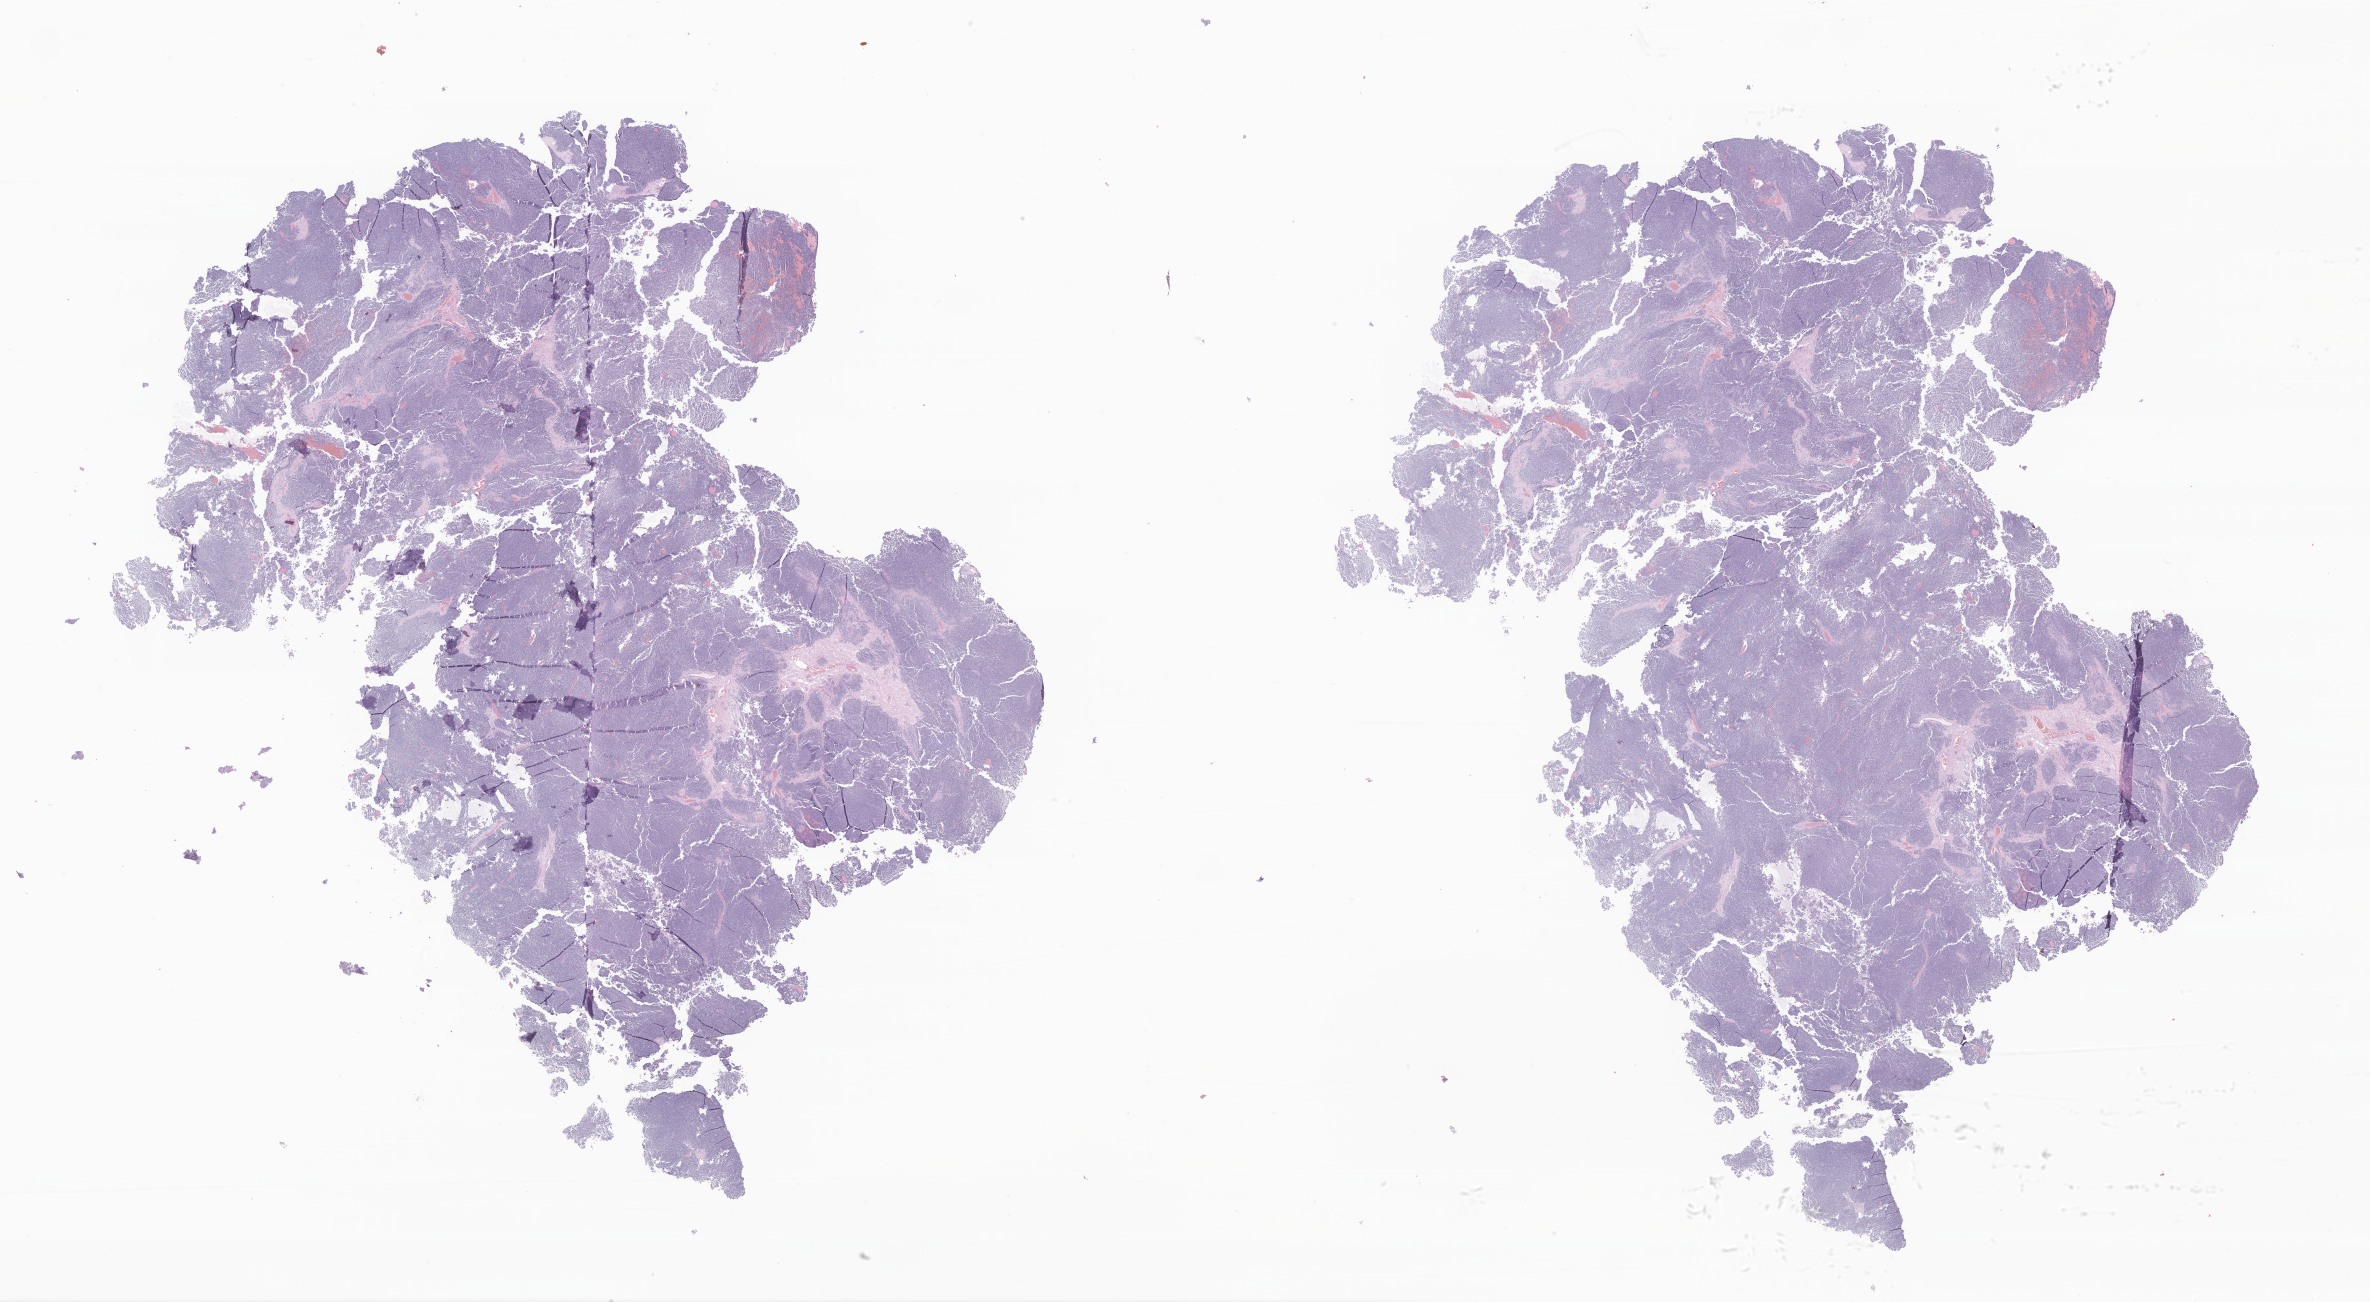
Digitized hematoxylin and eosin (H&E)-stained section of tumor tissue from the brain, a low-resolution overview of the entire scanned area, about 40.0 x 22.0 mm; formalin-fixed paraffin-embedded section. Female patient, age 99 months (8 years 3 months).
Diagnosis (ICD-O-3 morphology term): Tumor cells, uncertain whether benign or malignant.